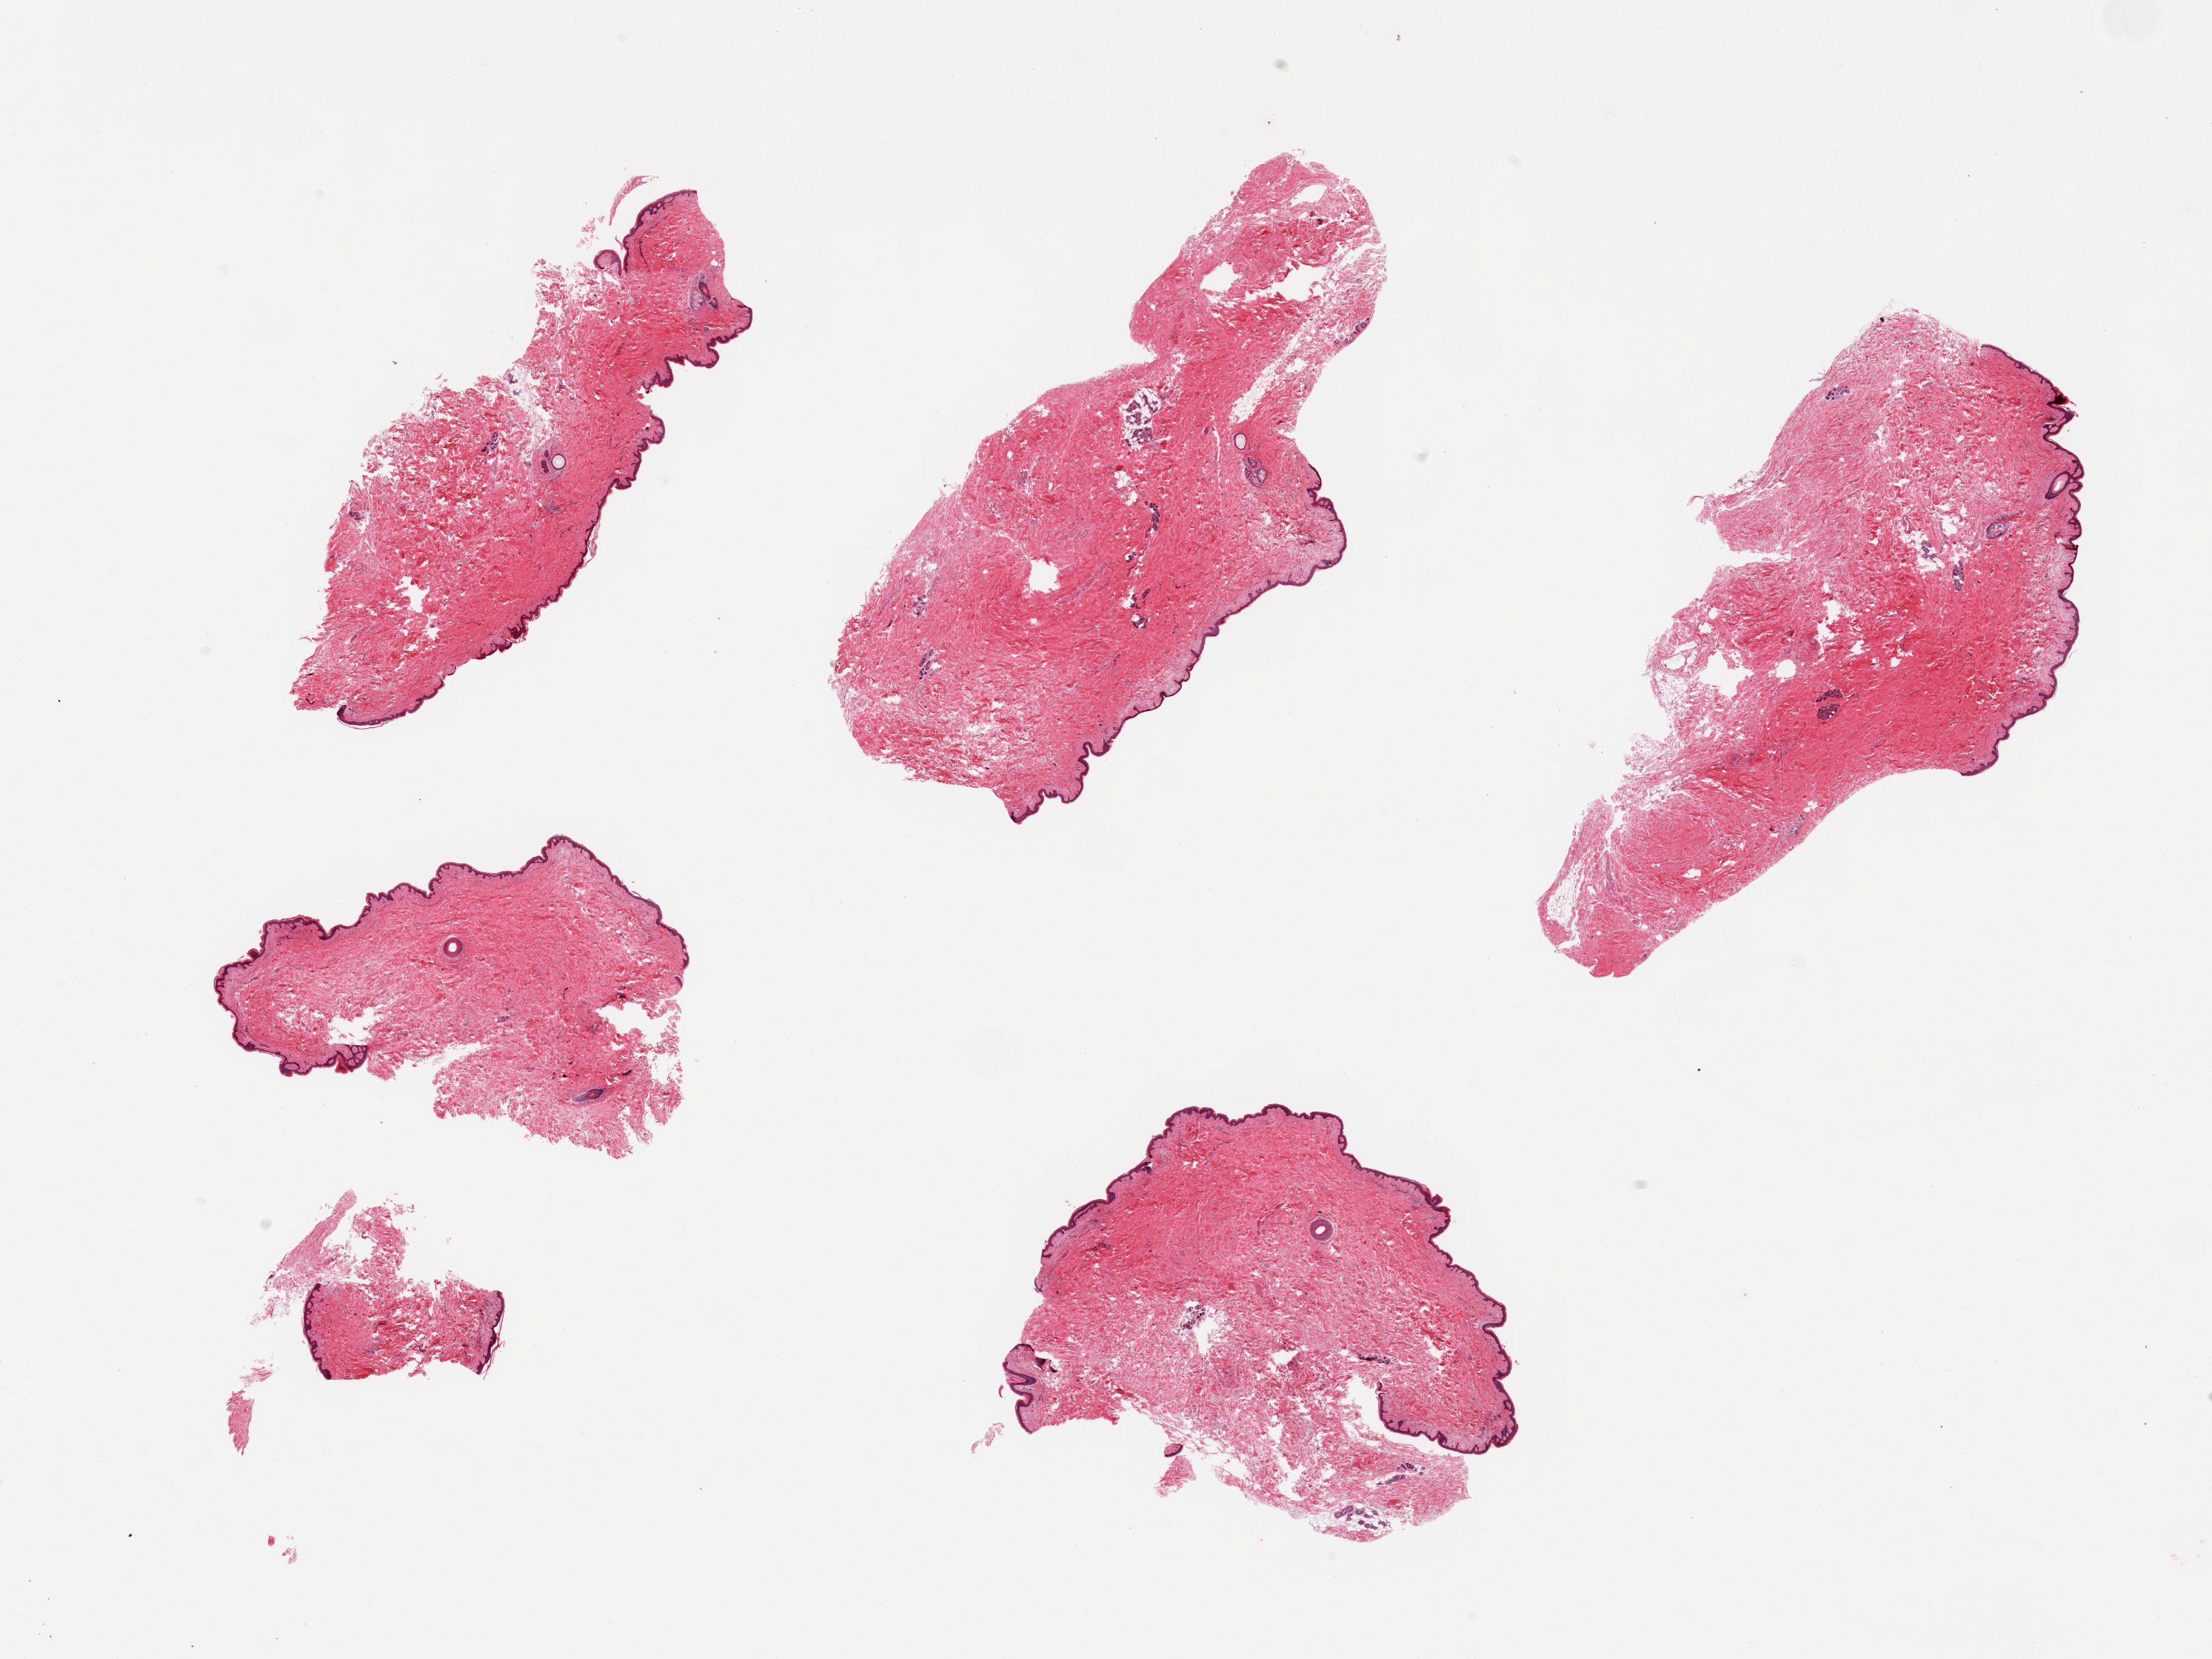
Haematoxylin and eosin whole-slide image, brightfield — a low-resolution overview of the entire scanned area, about 23.6 x 17.7 mm. PAXgene-fixed, paraffin-embedded tissue. Sampled site (target tissue): skin of suprapubic region. Tissue donor sample. Female donor.
Review note (as recorded): 6 pieces; insignificant amount of internal fat (periadnexal).